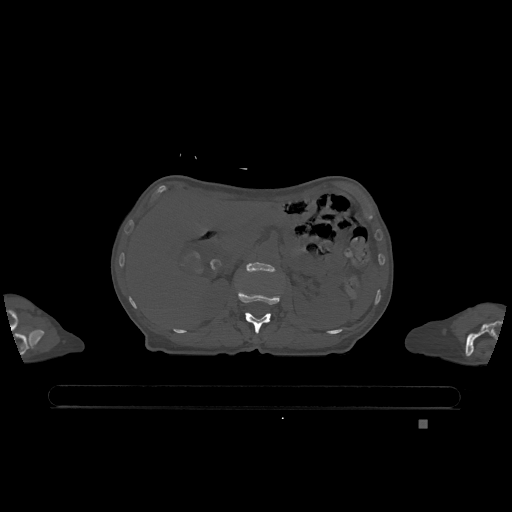
CT including the spine, one axial slice. Position 464 of 1317 along the scan axis. Bone window (W 1800 / L 400 HU). 512 × 512 image matrix, field of view 500 × 500 mm. Patient: female, 74 years. From the clinical record (not read from this slice): primary cancer: lung.
Annotated regions visible in this slice (semi-automatically segmented with operator editing):
- L1 vertebra: bounding box <238,290,281,333> (left, top, right, bottom; pixels)
- L2 vertebra: <246,262,275,272>